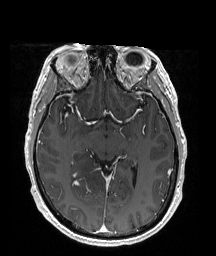
Brain MRI from a brain-tumour surgery series, one axial slice. Slice 106 of 176 in the series (ordered by position). T1-weighted post-contrast. 1 mm slice thickness. 216 × 256 image matrix, field of view 211 × 250 mm. From the clinical record (not read from this slice): histopathology: Oligodendroglioma; WHO grade: 2; IDH mutation: yes; tumour location: Right Parietal.
Outlined on this slice (manually delineated by an expert):
- tumour: bounding box <70,150,111,205> (left, top, right, bottom; pixels)